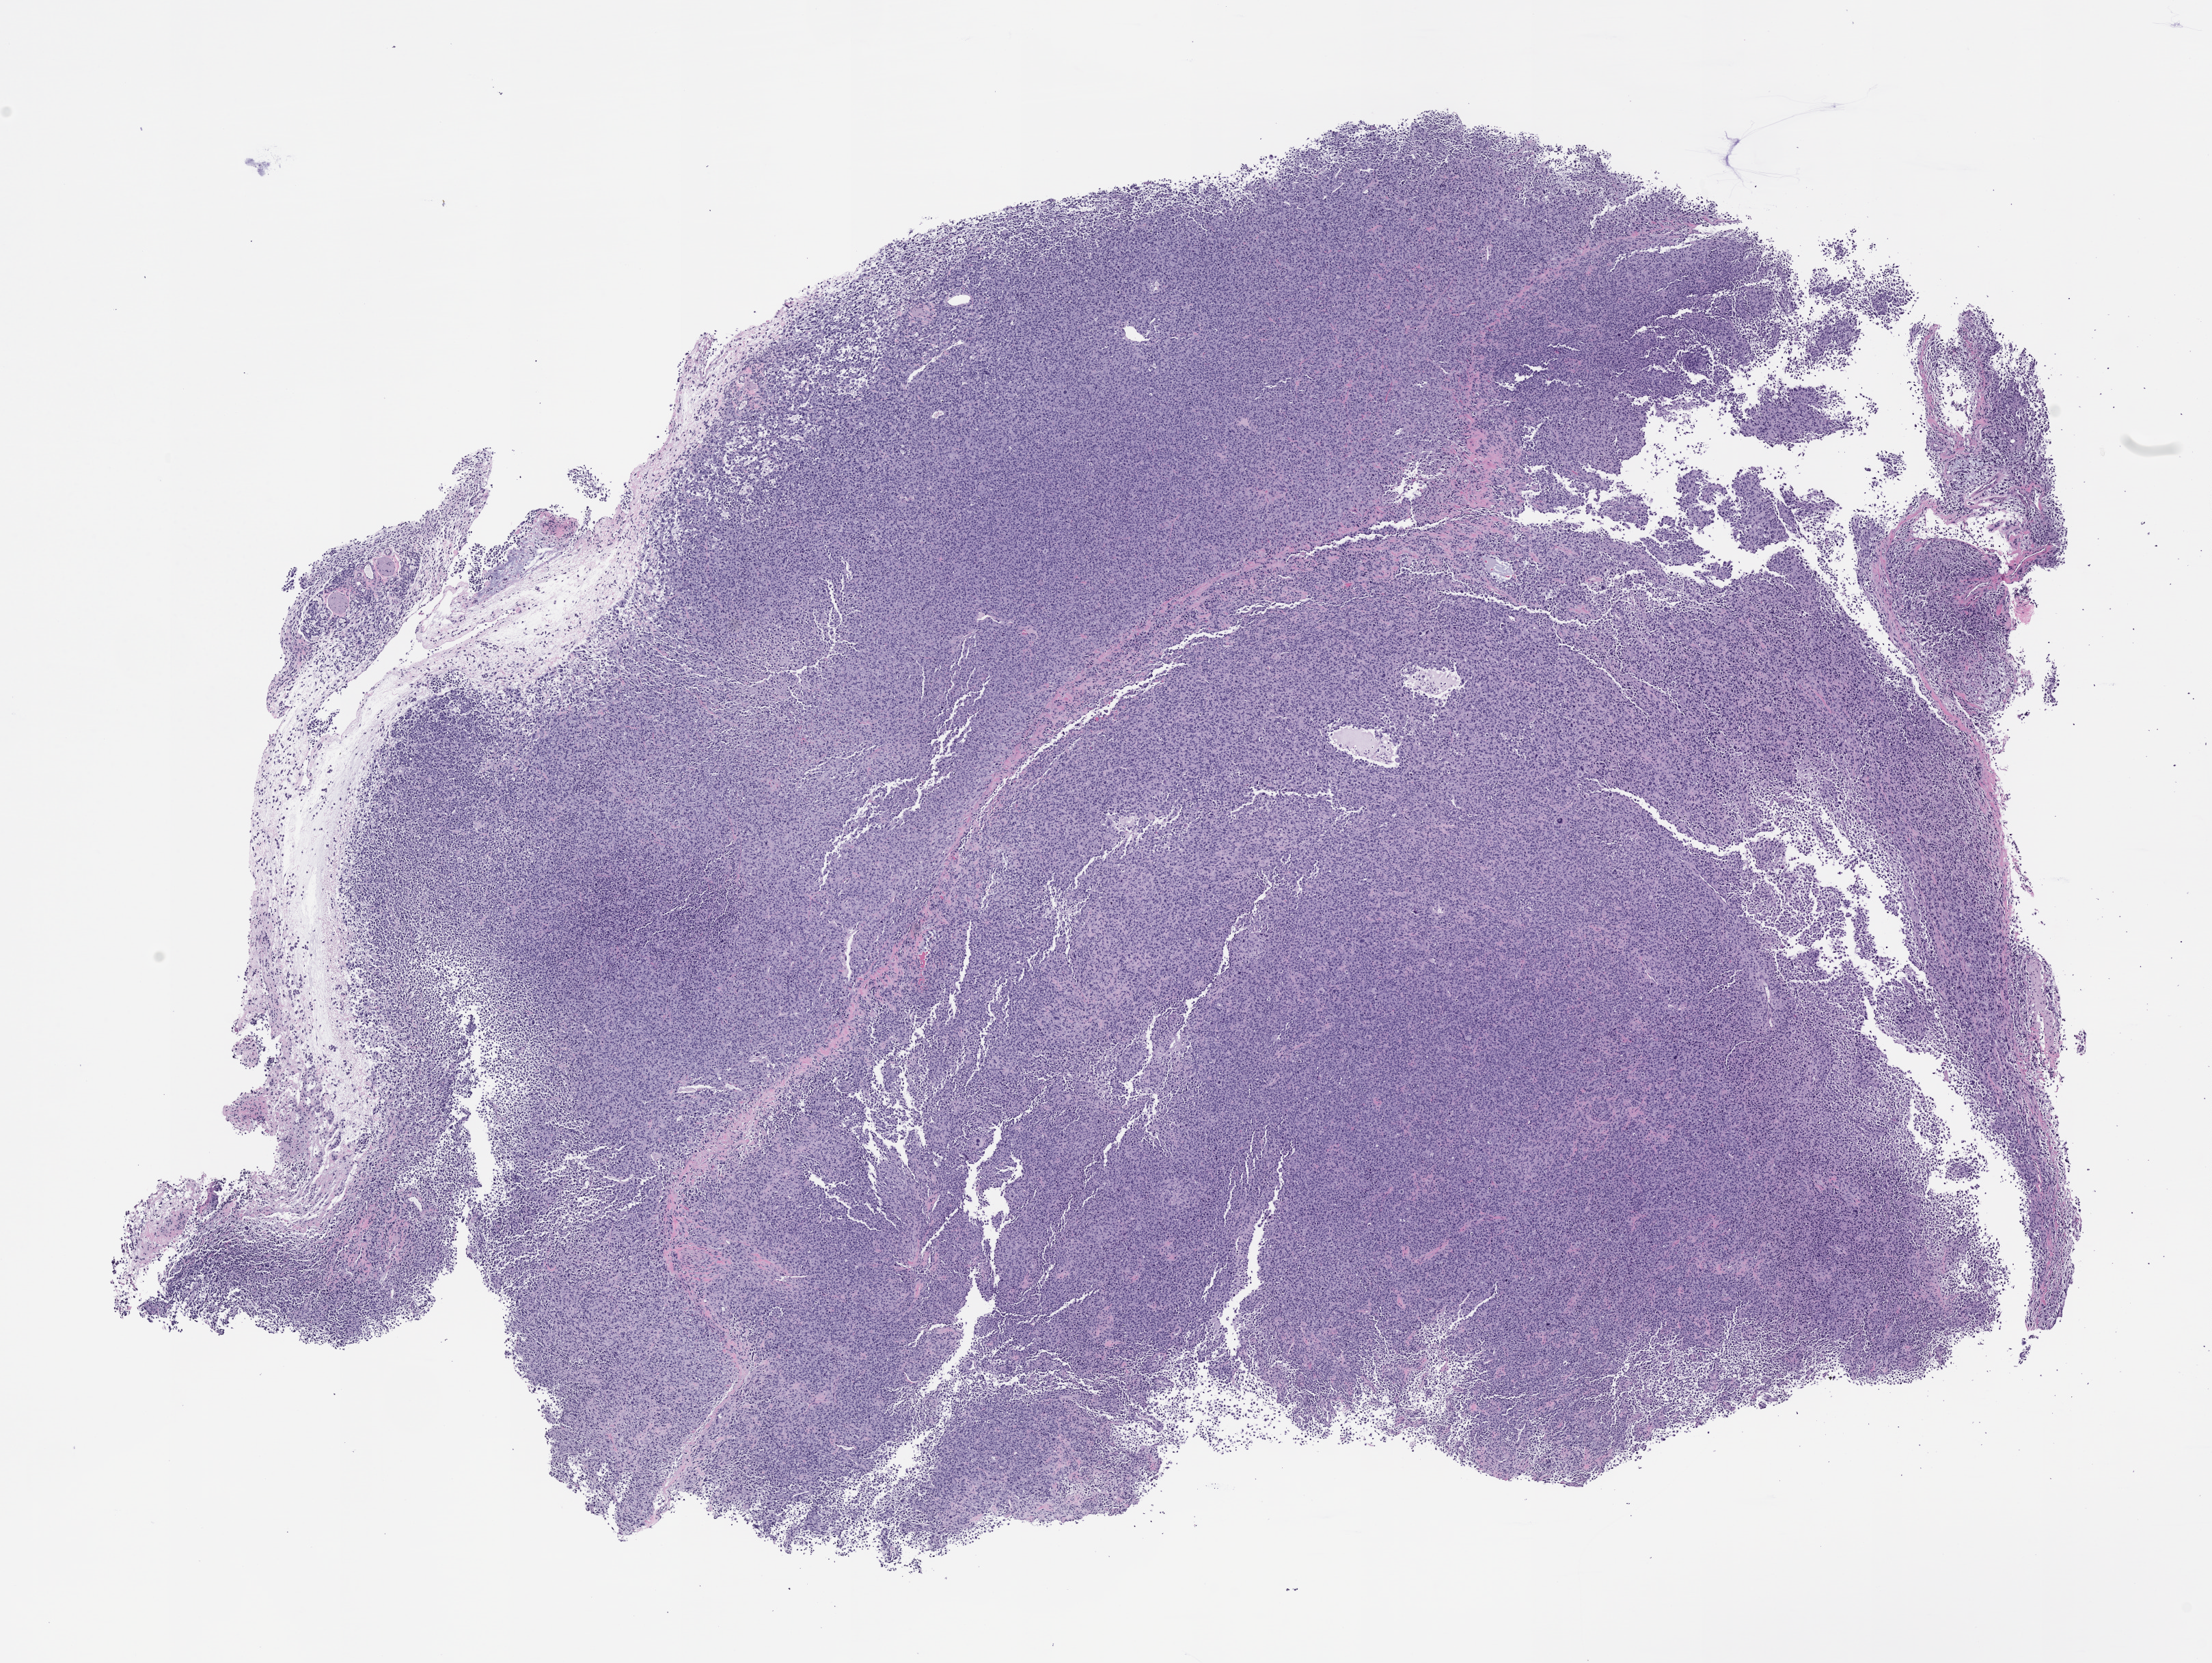
H&E whole-slide image of a patient-derived xenograft (PDX) tumor grown in a mouse, passage 0, shown as a low-resolution overview of the whole scanned area (about 13.0 x 9.8 mm); formalin-fixed paraffin-embedded section; originating tumor site category: musculoskeletal.
Originating patient diagnosis: Rhabdomyosarcoma.